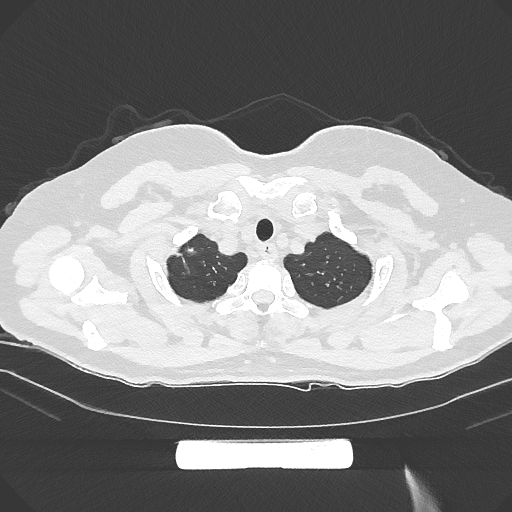
Chest CT, one axial slice. Slice 267 of 294 in the series (ordered by position). Reconstruction kernel IMR1,SharpPlus. Lung window (W 1500 / L -600 HU). 1 mm slice thickness. 512 × 512 image matrix. Patient: female, 58 years. Case-level facts recorded for this patient, not image findings: clinical TNM (as recorded): T1b N0 M0; histopathological grade: G2-3.
Annotated regions visible in this slice (rectangle marked by the reading radiologist):
- lung tumour (recorded histology: adenocarcinoma): bounding box [x1, y1, x2, y2] px = [172, 247, 202, 280]